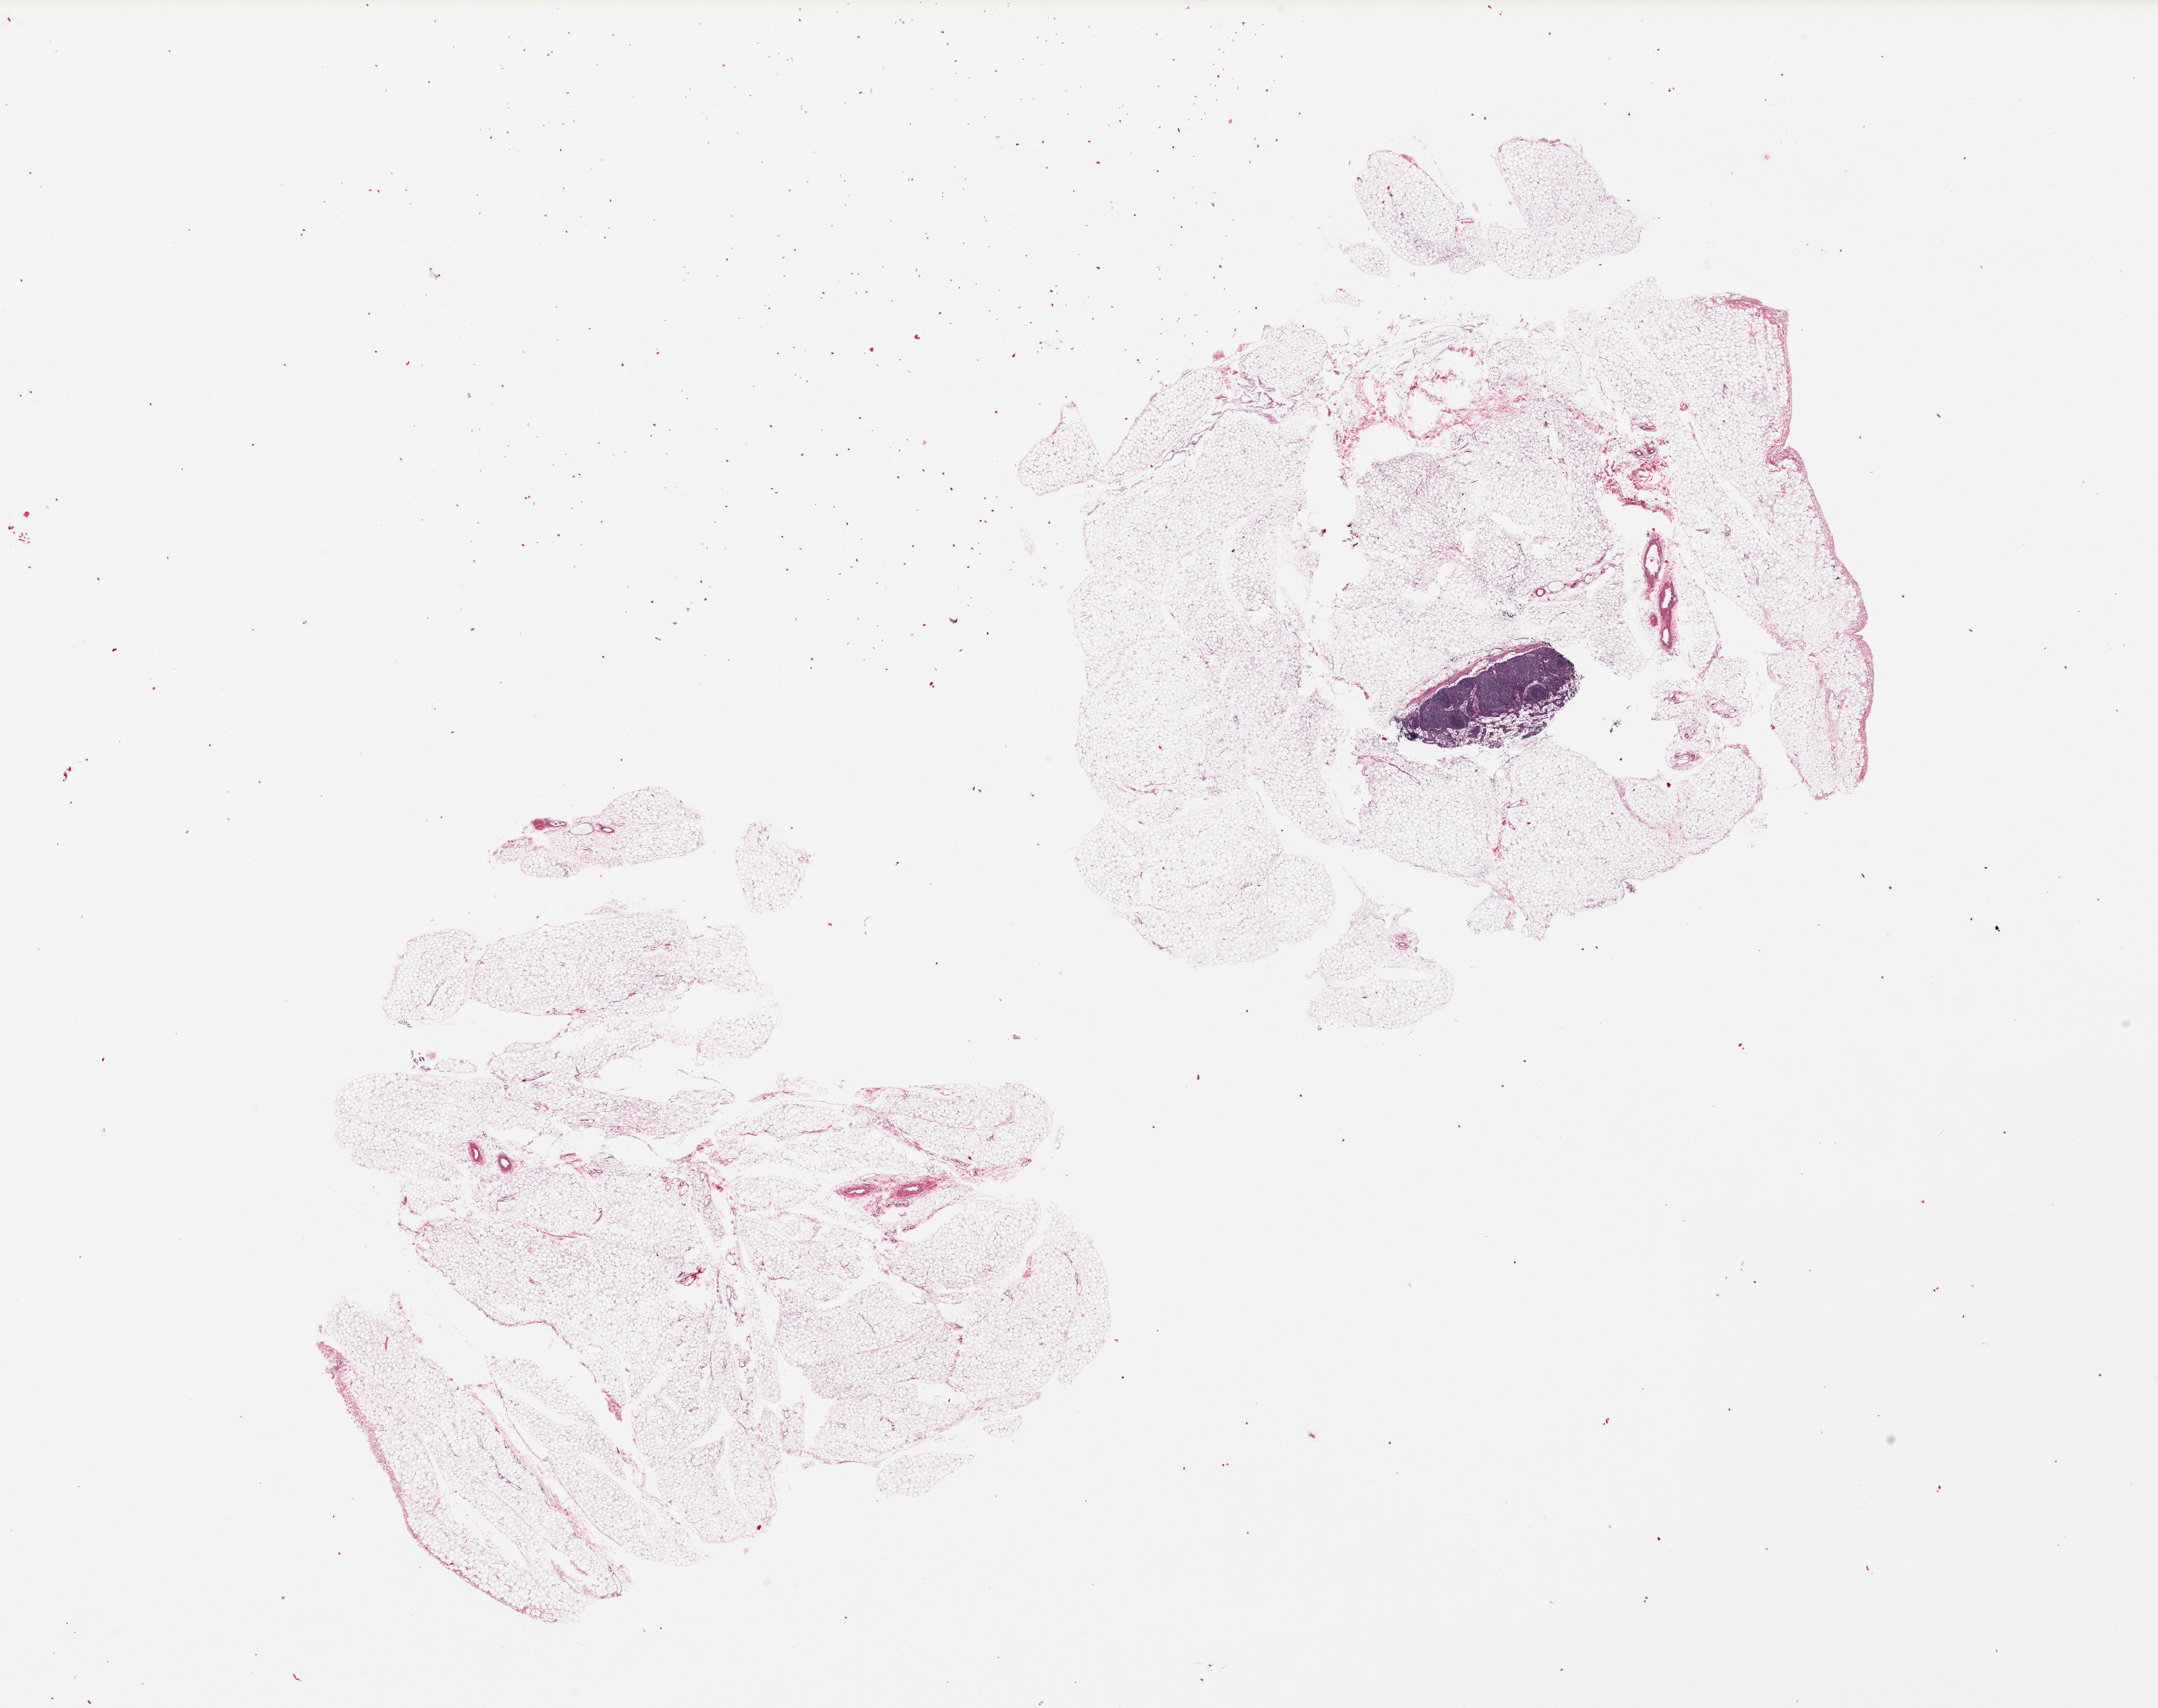
Haematoxylin and eosin whole-slide image, brightfield — shown as a low-resolution overview of the whole scanned area (about 27.6 x 21.8 mm). Male donor.
Specimen: PAXgene-fixed paraffin-embedded (PFPE) section; target tissue: omentum; donor tissue sample.